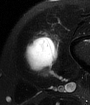
MRI of an extremity soft-tissue mass, one axial slice. Slice 17 of 65 in the series (ordered by position). T2-weighted fat-saturated. MR volume resampled by the dataset authors to the PET/CT grid (not the native acquisition matrix). 3.27 mm slice thickness. 90 × 105 image matrix, field of view 88 × 103 mm. Male patient. From the clinical record (not read from this slice): histological type: mixoid liposarcoma; grade: low; site of the primary tumour: left thigh.
Outlined on this slice (expert contour drawn on MRI and transferred to this co-registered scan by the dataset authors):
- gross tumour volume (mass): bounding box [x1, y1, x2, y2] px = [23, 34, 58, 72]